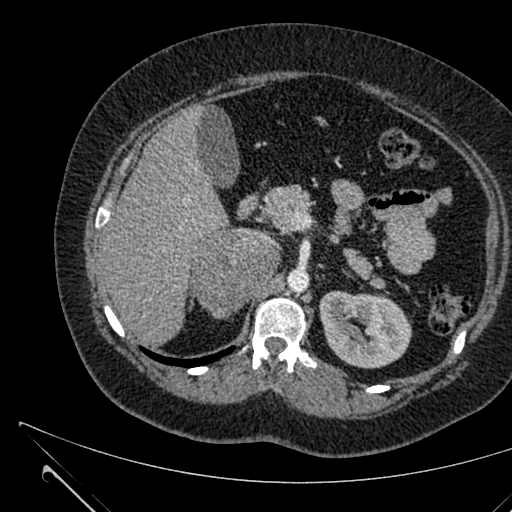
Contrast-enhanced abdominal CT, one axial slice. Slice 409 of 731 in the series (ordered by position). 120 kVp. Intravenous contrast given. Soft-tissue window (W 400 / L 40 HU). 1 mm slice thickness. 512 × 512 image matrix. Patient: female, 36 years. From the clinical record (not read from this slice): diagnosis: adrenocortical carcinoma; tumour side: right adrenal; tumour size at pathology: 10 cm; Ki-67 index: 20 %; stage (as recorded): 4.
Outlined on this slice (semi-automatically segmented with operator editing):
- mass: bounding box [x1, y1, x2, y2] px = [190, 230, 275, 316]